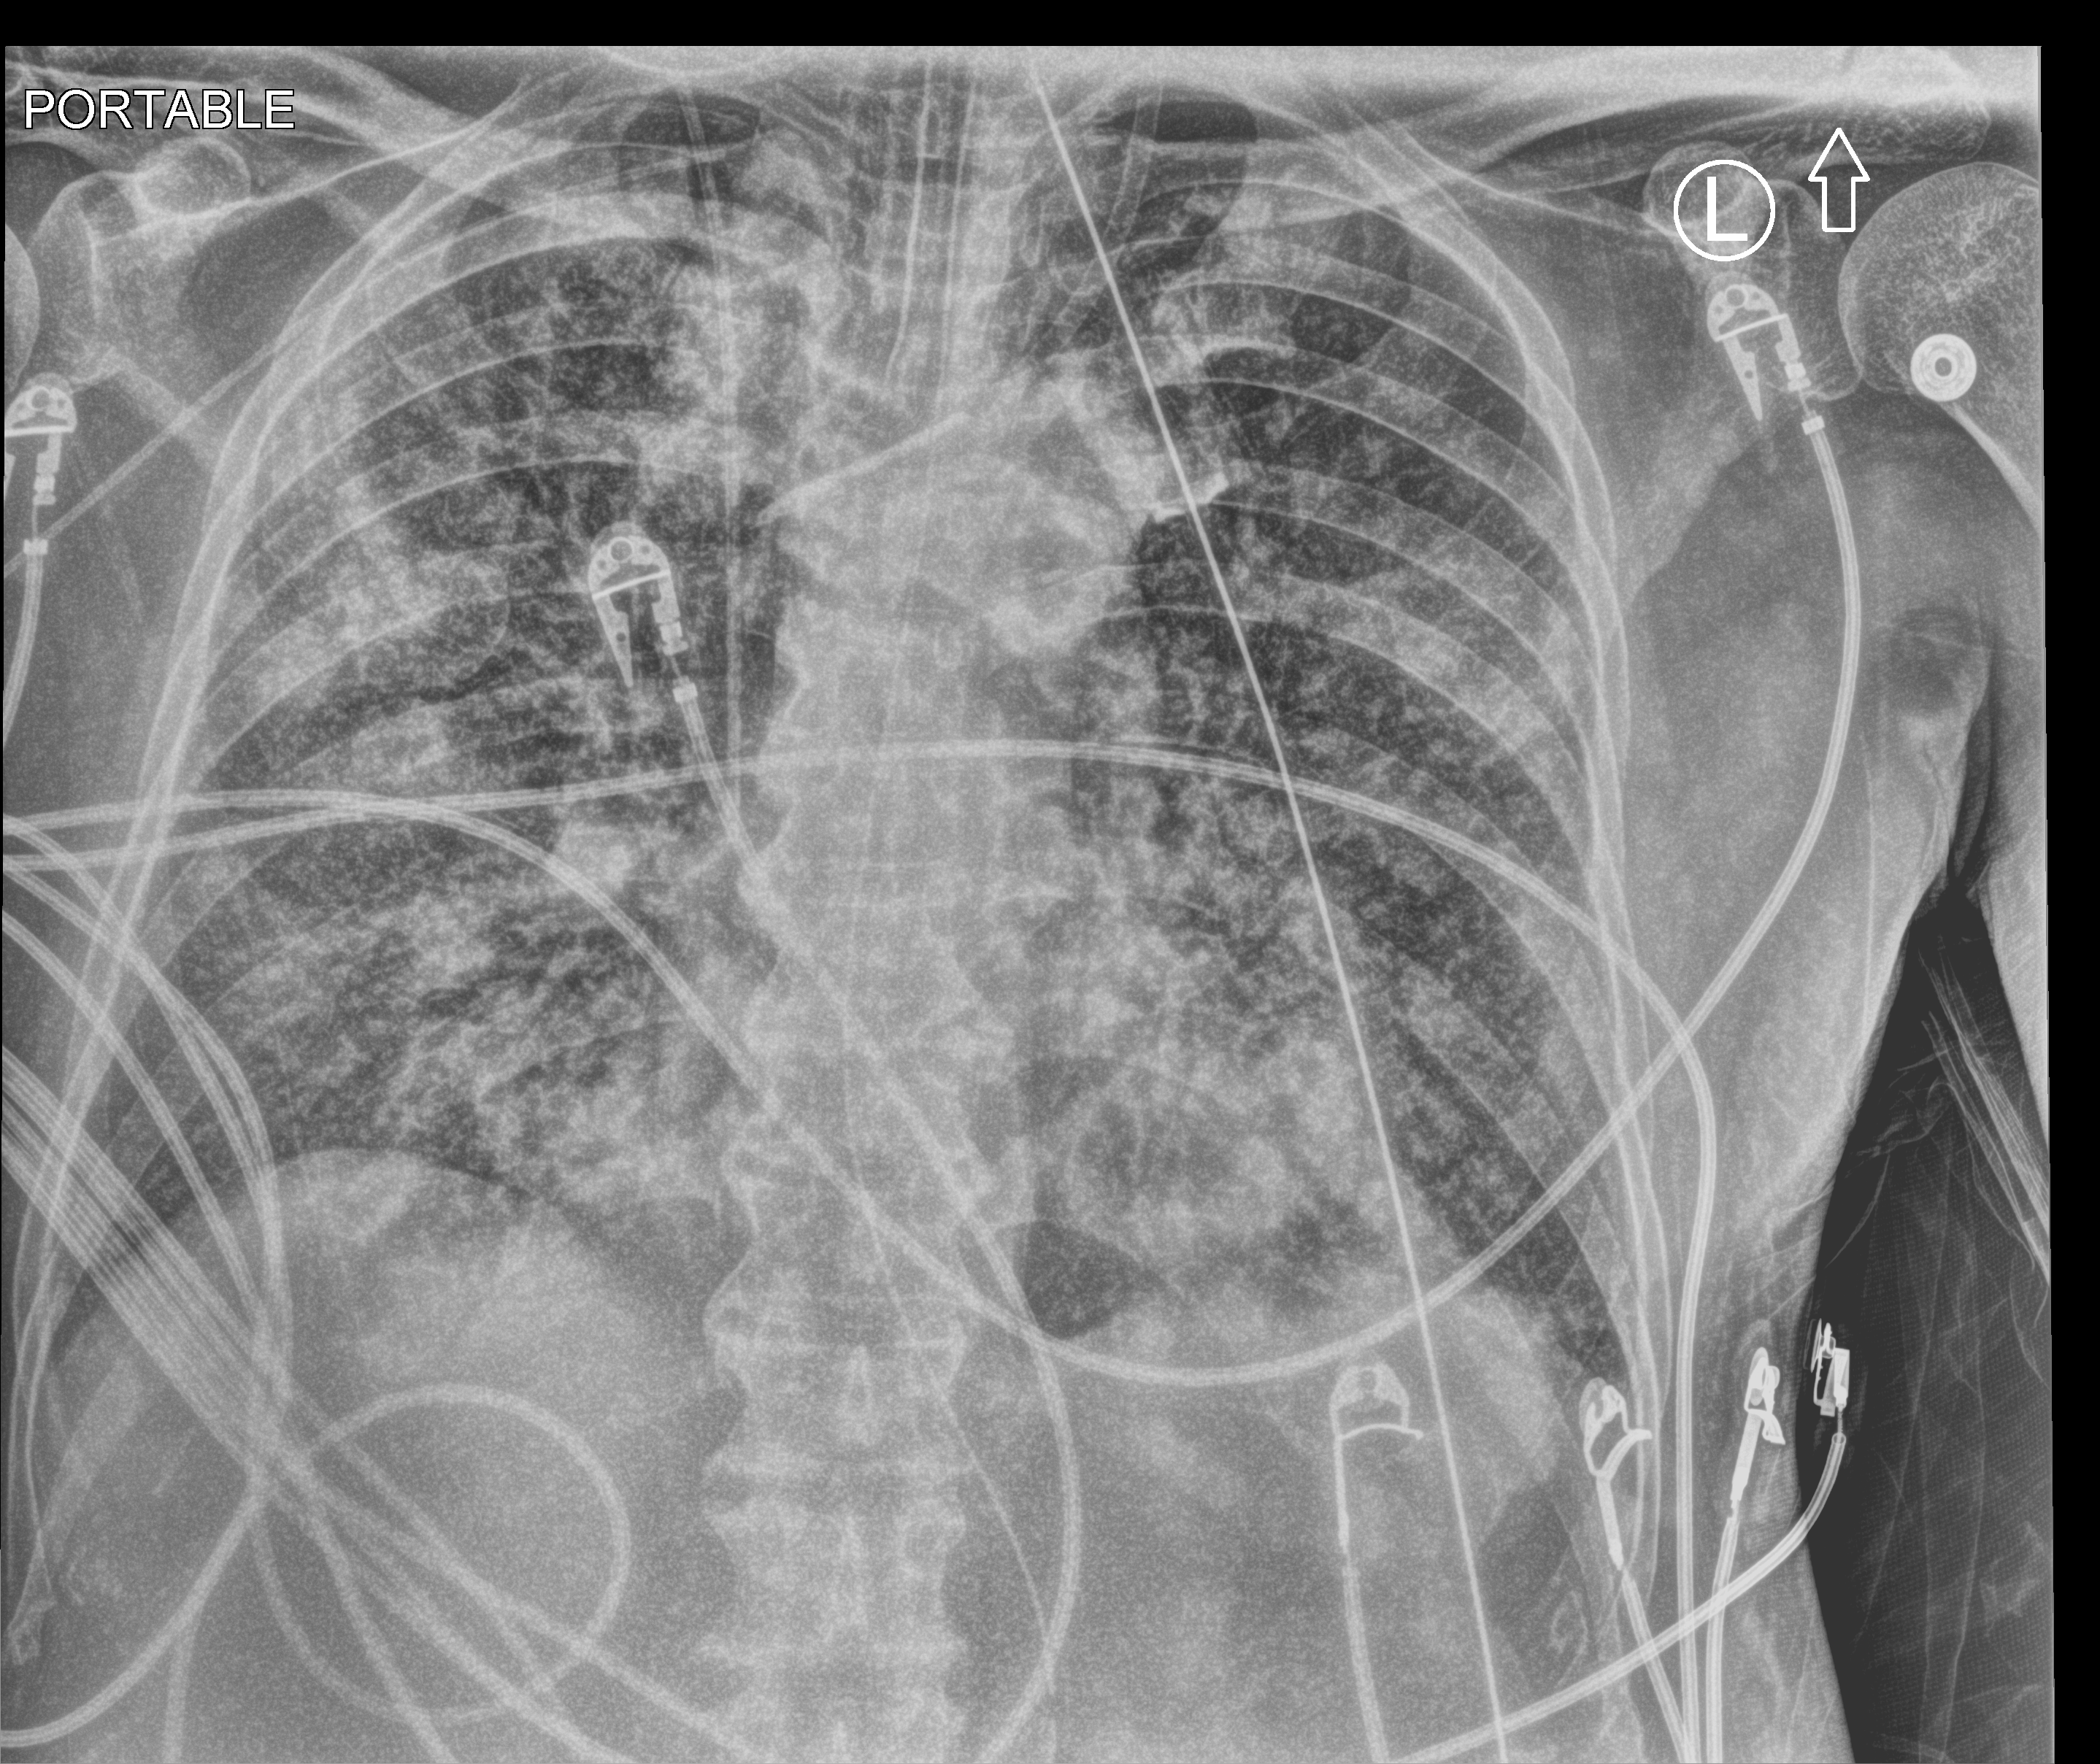
Bedside chest radiograph (computed radiography); anteroposterior (AP) projection. Male patient hospitalised with COVID-19, age 60–74 years.
Hospital-stay facts (about this admission, not read from this image; timing relative to this image not recorded):
- admitted to intensive care during this hospital stay: yes
- diabetes (admission record): no
- mechanically ventilated during this hospital stay: yes